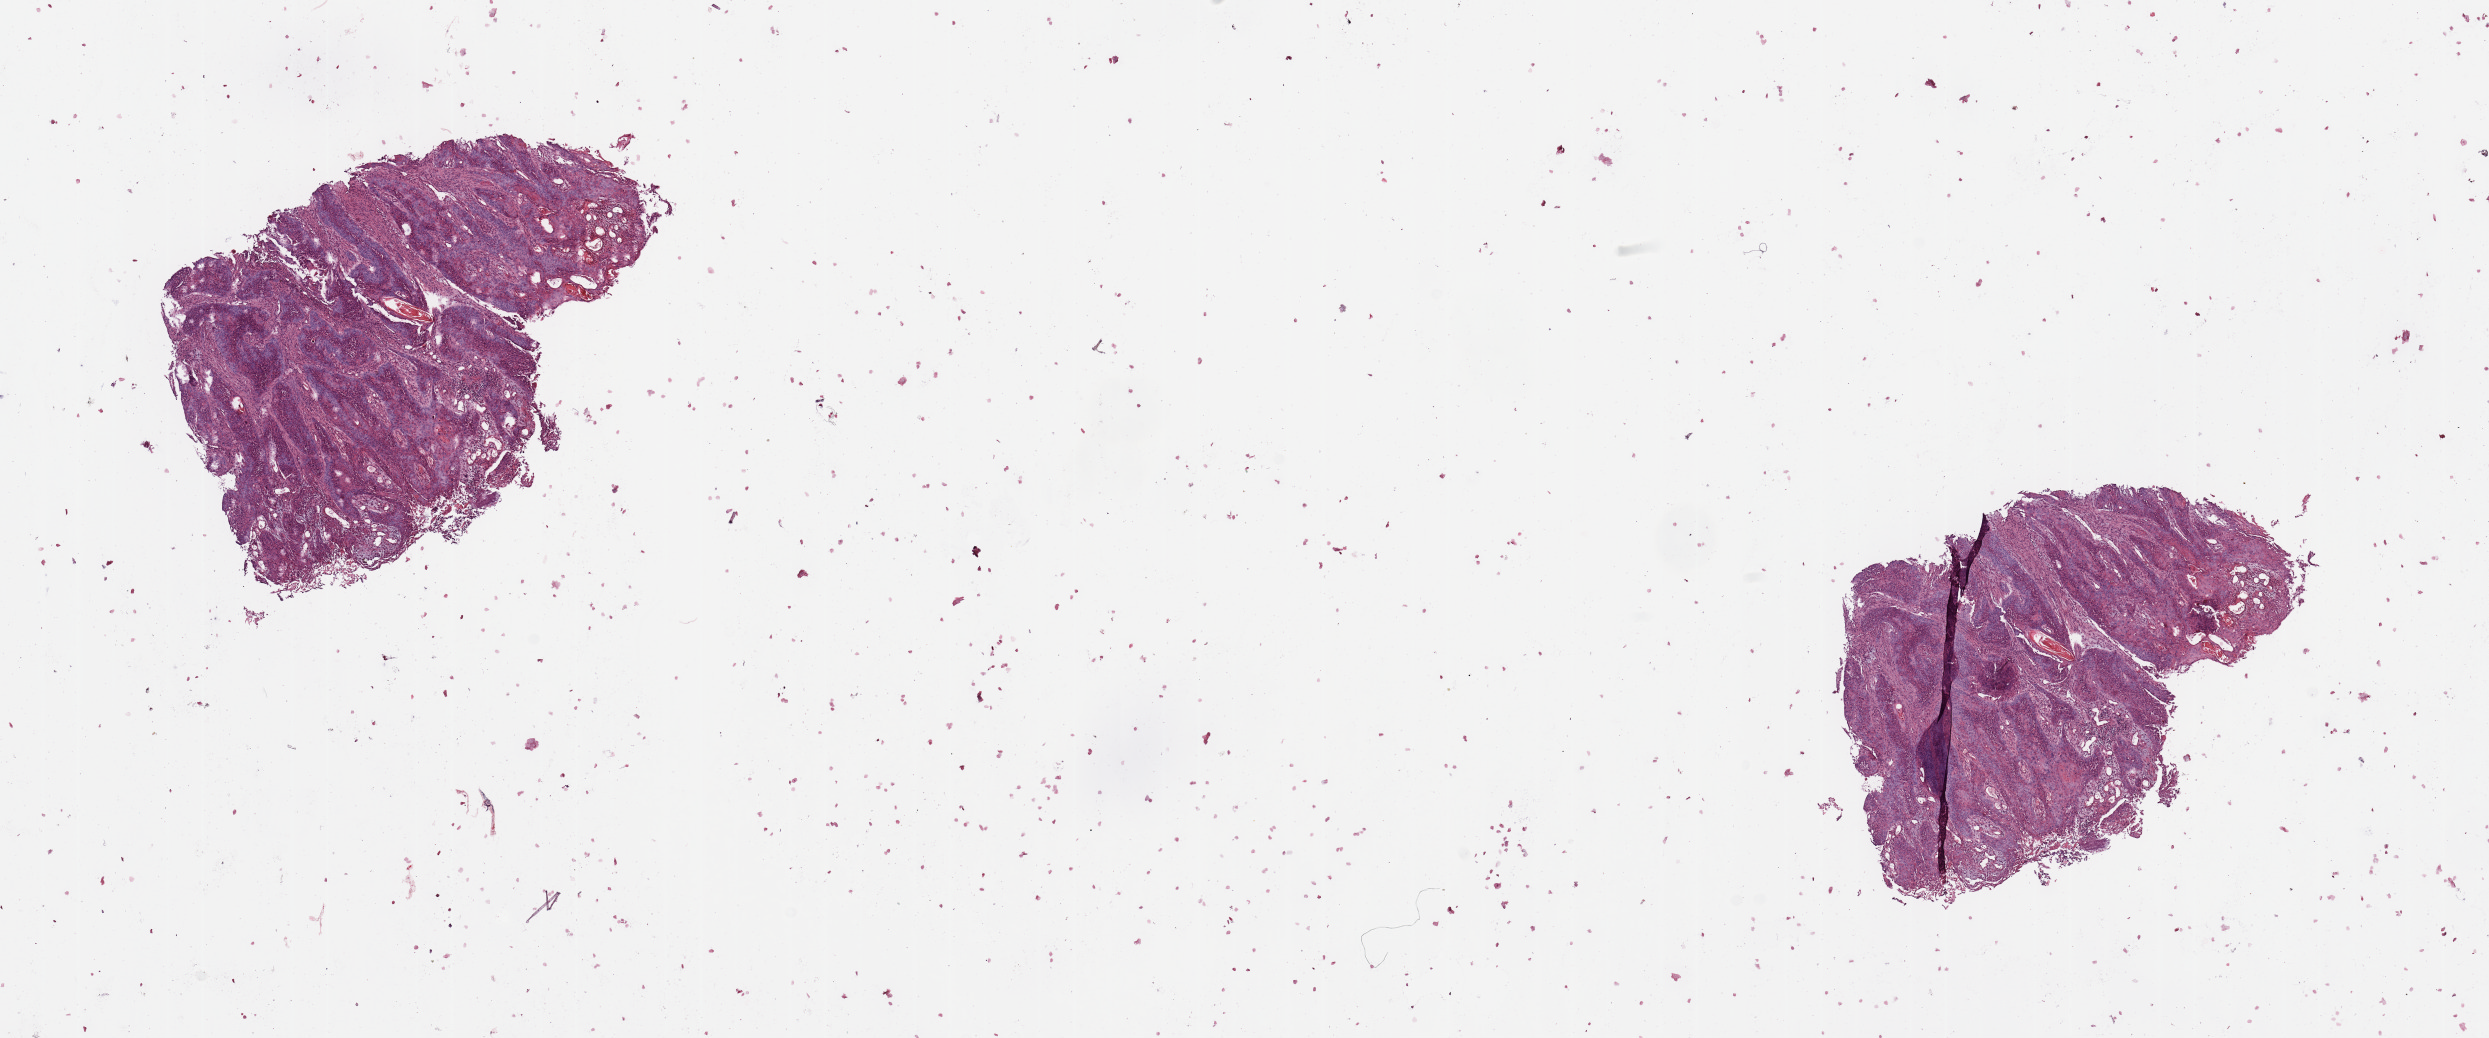
H&E-stained whole-slide image — low-resolution overview of the scanned area, about 19.7 x 8.2 mm (from a 20x scan), tumour tissue sample, sampled site: larynx. 50-year-old male patient. Histologic grade: G2 (moderately differentiated). Pathologist review of this section (percent, as recorded): tumour nuclei 80%, necrosis 5%.
- diagnosis: Squamous cell carcinoma, NOS (larynx, NOS)
- AJCC pathologic stage: III